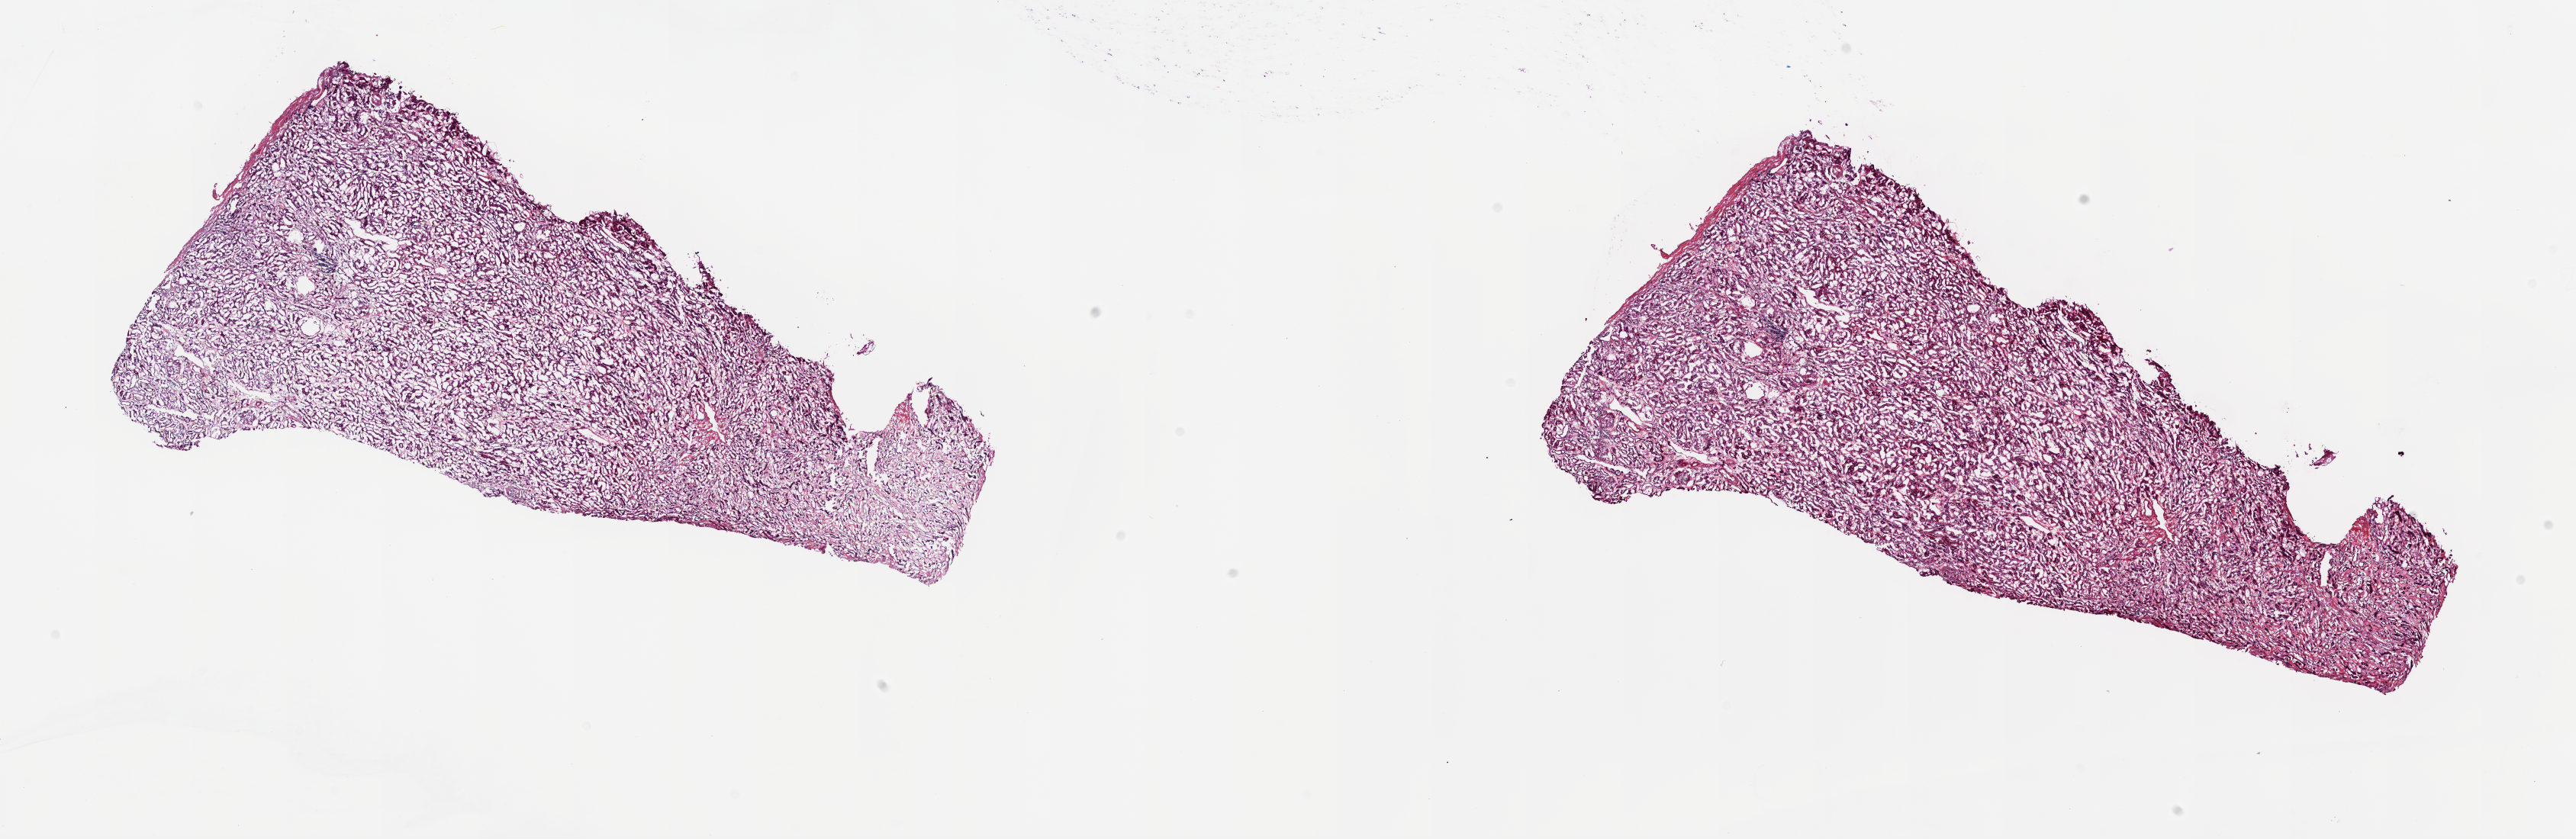
H&E whole-slide image, shown as a low-resolution overview of the whole scanned area (about 26.8 x 8.7 mm, acquisition: 20x scan); frozen section; solid tissue normal (non-tumour tissue) sample from the kidney. Male patient; age at initial diagnosis 70 years. Slide review estimates, as recorded: tumour cells 0%, tumour nuclei 0%, normal cells 55%, stromal cells 45%, necrosis 0%. Inflammatory infiltration, as recorded: lymphocyte infiltration 4%, monocyte infiltration 2%, neutrophil infiltration 0%.
This section: solid tissue normal (non-tumour) sample from the same patient. Patient diagnosis: Papillary adenocarcinoma, NOS.